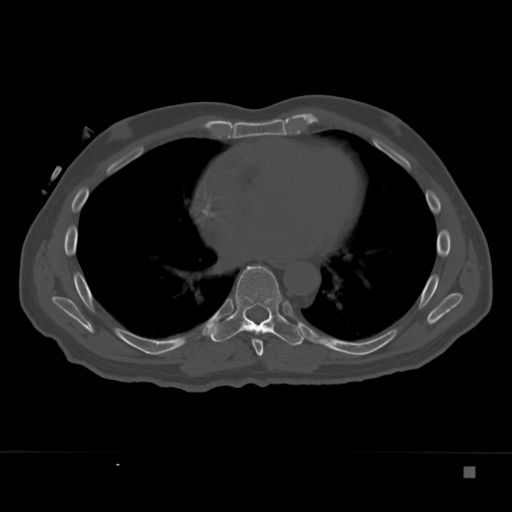
CT including the spine, one axial slice; position 211 of 332 along the scan axis; reconstruction kernel Br40s; 120 kVp; bone window (W 1800 / L 400 HU); 1.5 mm slice thickness; 512 × 512 image matrix. Male patient, age 72 years. Case-level facts recorded for this patient, not image findings: primary cancer: skeletal.
Structures marked on this image (semi-automatic segmentation, software-assisted and operator-edited):
- T7 vertebra: bounding box (x1, y1, x2, y2) in pixels: (252, 339, 264, 357)
- T8 vertebra: (211, 266, 307, 346)